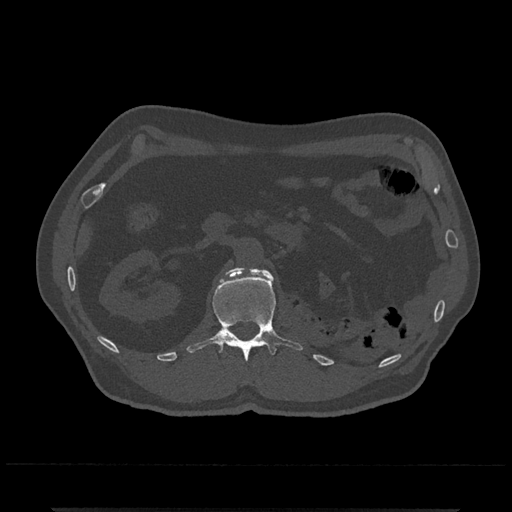
CT including the spine, one axial slice; slice 357 of 797 in the series (ordered by position); reconstruction kernel Br40s/3; bone window (W 1800 / L 400 HU); 512 × 512 image matrix, field of view 393 × 393 mm. Patient: male, 67 years. From the clinical record (not read from this slice): primary cancer: prostate.
Structures marked on this image (semi-automatic segmentation, software-assisted and operator-edited):
- L1 vertebra: bounding box [x1, y1, x2, y2] px = [186, 267, 303, 362]